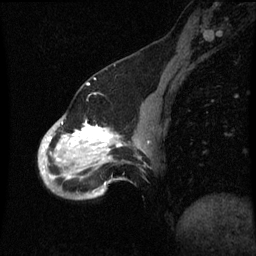
Breast MRI (dynamic contrast-enhanced), one sagittal slice; position 18 of 60 along the scan axis; dynamic contrast-enhanced series, image 2 of 3 at this slice position (ordered by acquisition); 1.5 T; TE 4.2 ms, TR 8.9 ms; 2 mm slice thickness; 256 × 256 image matrix, field of view 200 × 200 mm. Patient: female, 49 years. Case-level facts recorded for this patient, not image findings: setting: breast cancer imaged before/during neoadjuvant chemotherapy; receptor status: HR-positive, HER2-negative.
Outlined on this slice (semi-automatically segmented with operator editing):
- analysis volume of interest (the breast-tissue region the enhancement analysis was run in; not a lesion): bounding box (x1, y1, x2, y2) in pixels: (40, 100, 151, 199)
- tumour enhancement mask (voxels above the 70 % enhancement threshold inside the analysis volume of interest): (48, 126, 117, 179)